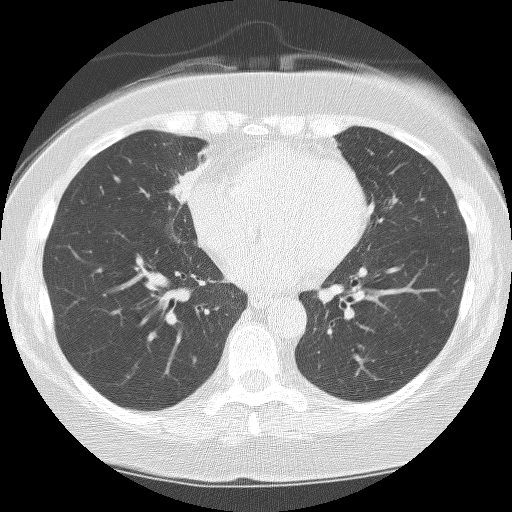
Low-dose screening chest CT, one axial slice; position 76 of 159 along the scan axis; reconstruction kernel BONE; 120 kVp; lung window (W 1500 / L -600 HU); 512 × 512 image matrix.
Outlined on this slice (manually delineated by an expert):
- lesion 1 (tumor, hilum of right lung): bounding box [x1, y1, x2, y2] px = [169, 146, 210, 204]